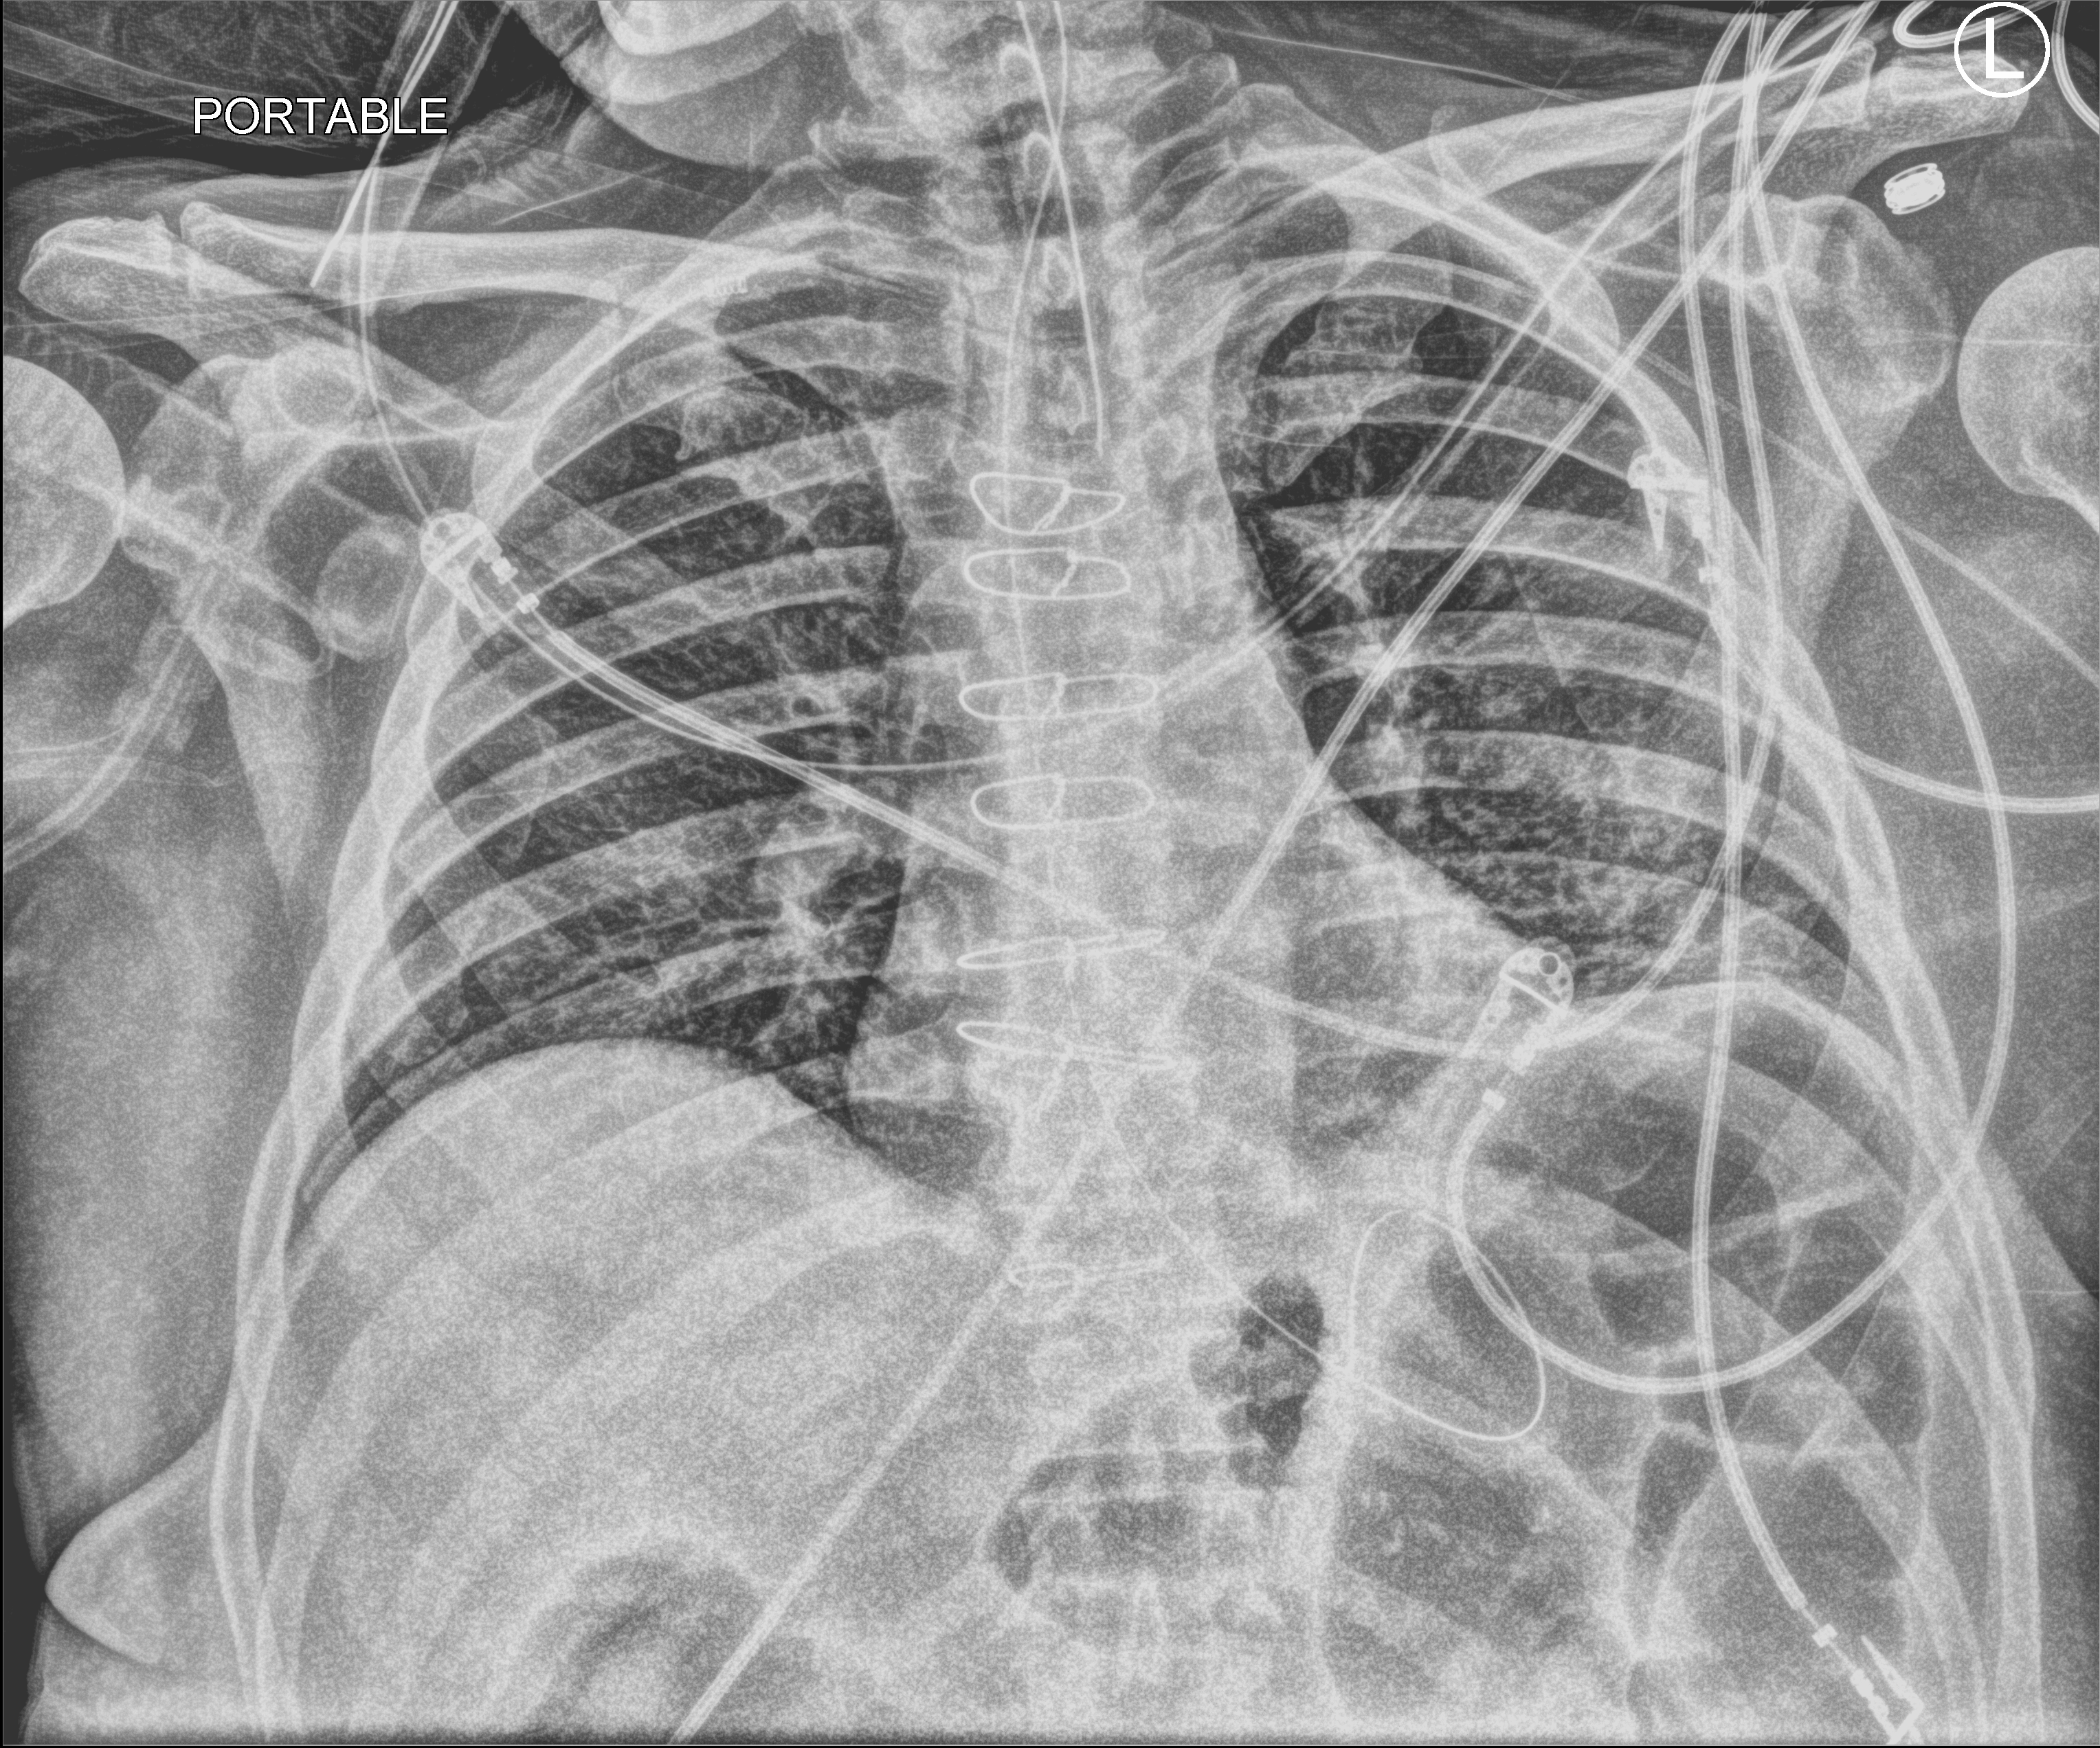
Chest X-ray (portable), anteroposterior (AP) projection. Patient hospitalised with COVID-19; male, aged 60–74 years.
Admission-level facts for this patient (not findings on this image; timing relative to this image not recorded): admitted to intensive care during this hospital stay: yes.